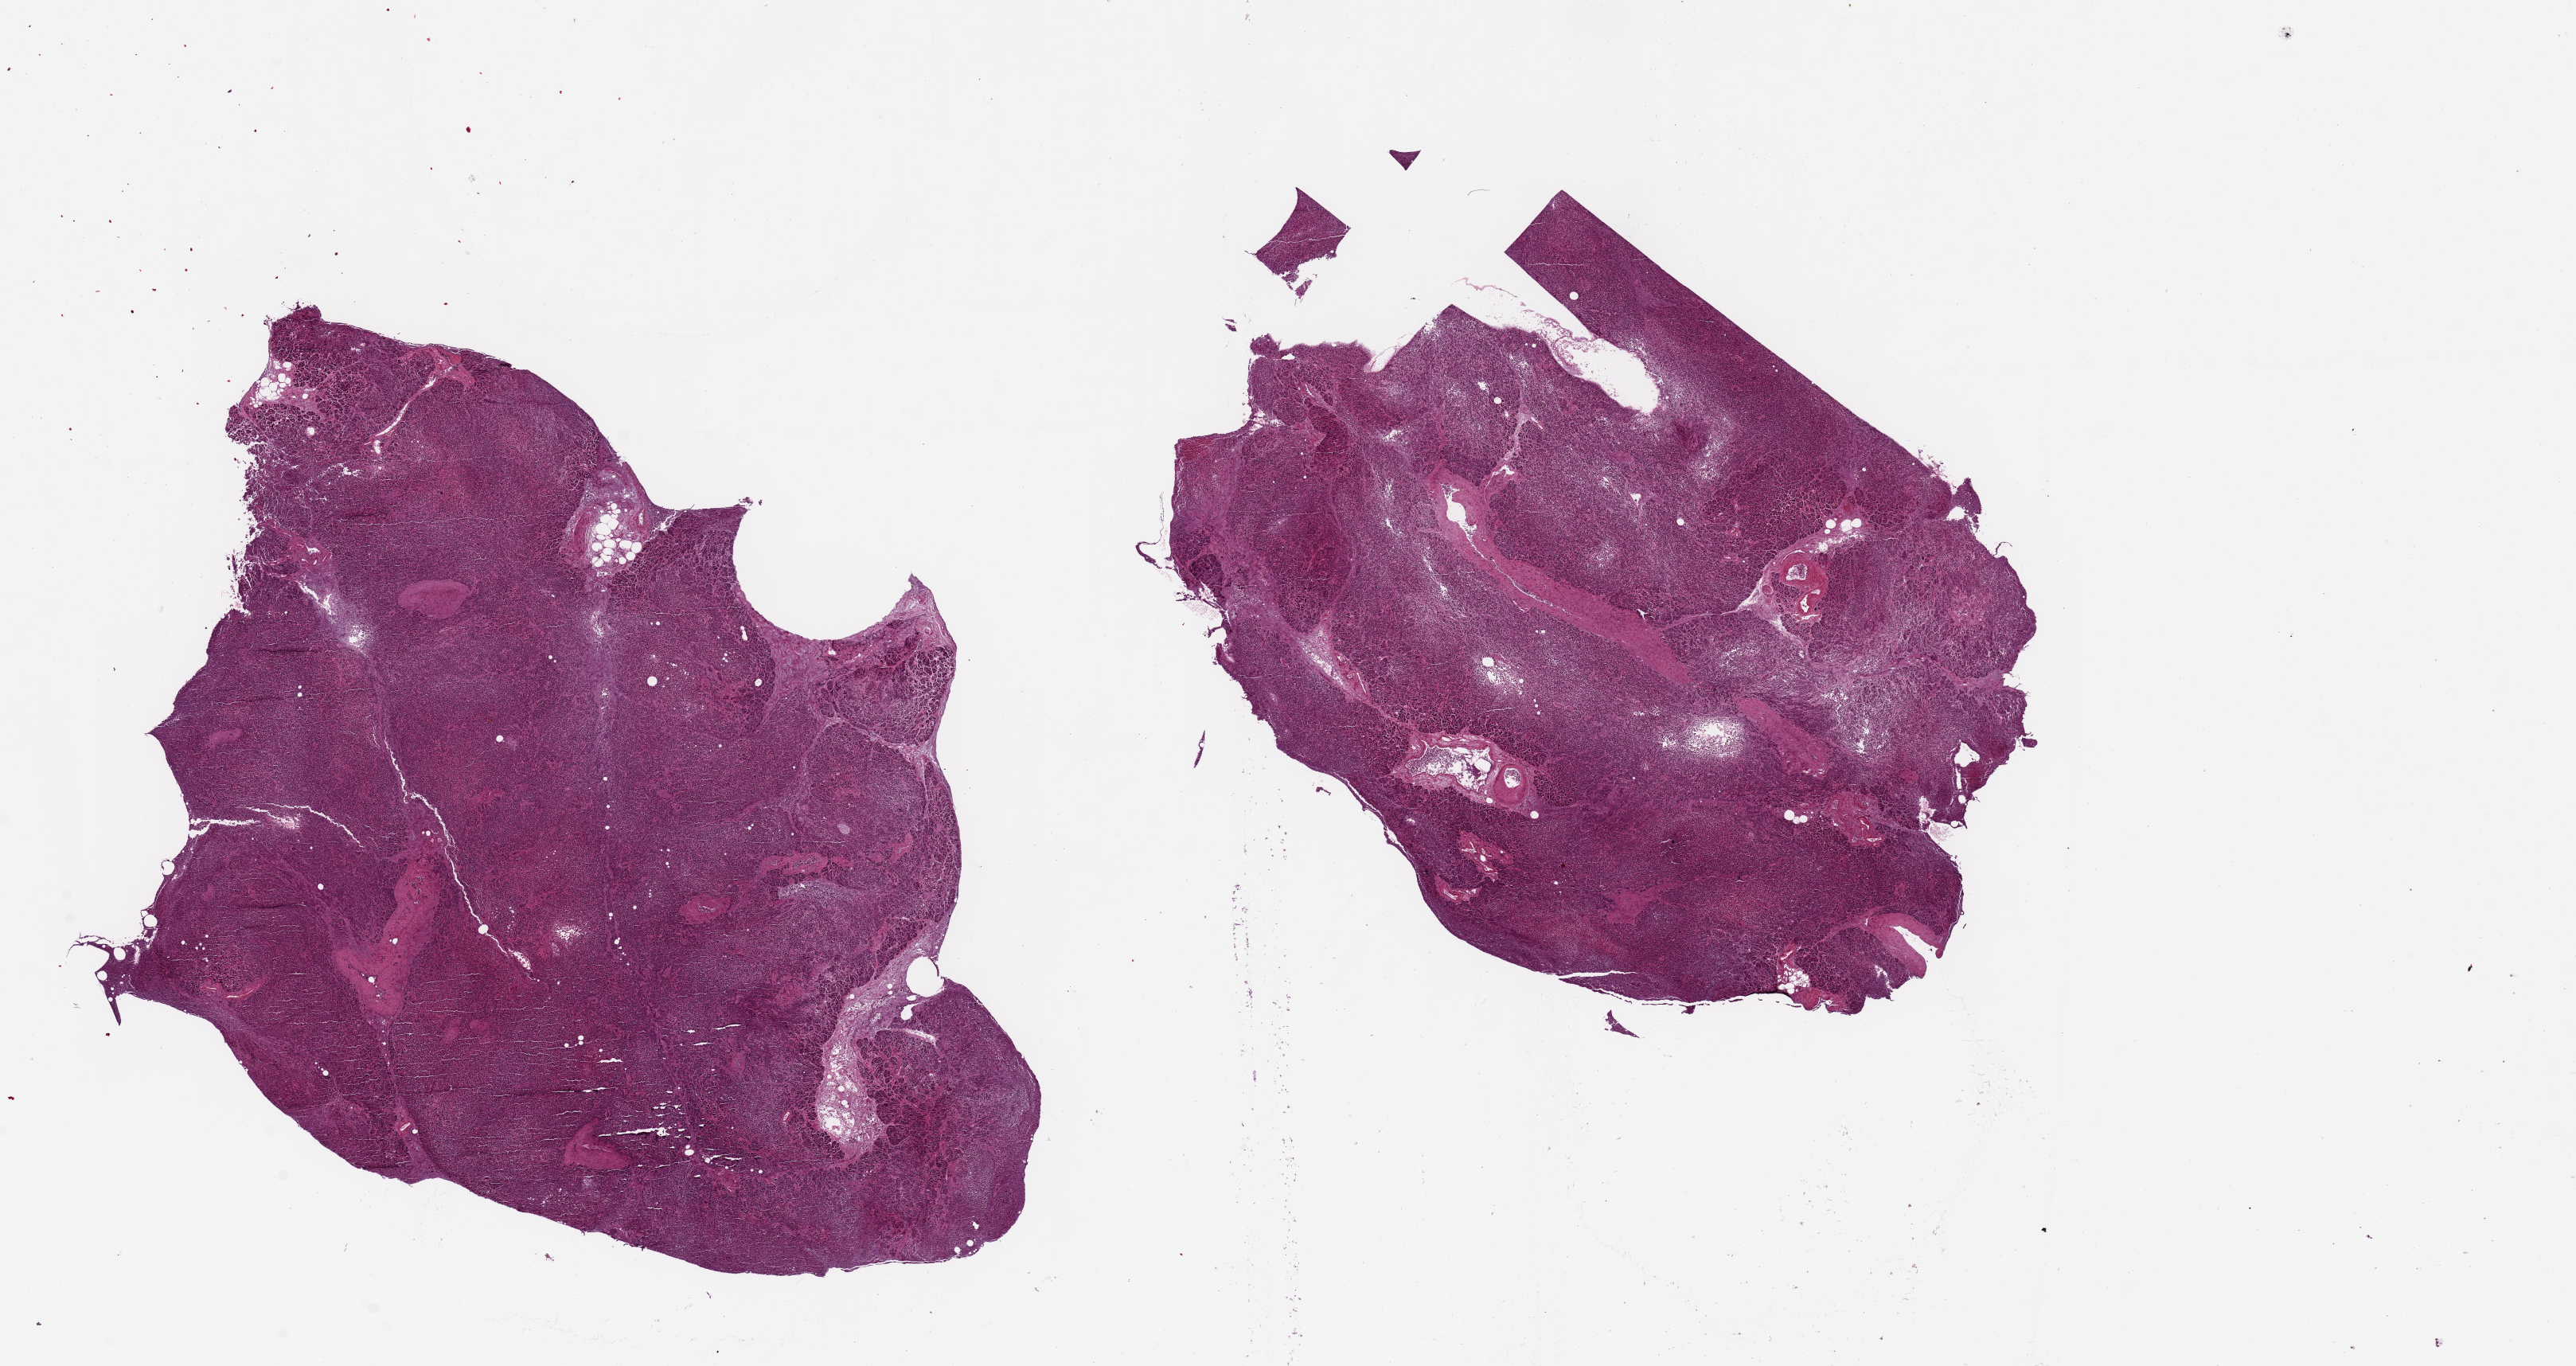
Hematoxylin and eosin (H&E) whole-slide image — shown as a low-resolution overview of the whole scanned area (about 25.6 x 13.6 mm, from a 20x scan), PAXgene-fixed, paraffin-embedded tissue, target tissue: pancreas, donor tissue sample. Female donor.
* pathologist's review note for this sample: 2 pieces, 11x10 & 9x7mm; badly saponified/autolyzed. Islets not well seen